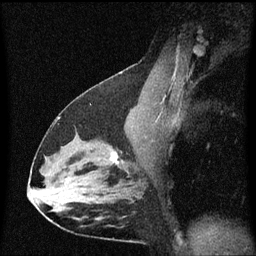
Breast MRI (dynamic contrast-enhanced), one sagittal slice; position 35 of 60 along the scan axis; dynamic contrast-enhanced series, image 2 of 3 at this slice position (ordered by acquisition); 1.5 T; TE 4.2 ms, TR 8.4 ms; 2 mm slice thickness; 256 × 256 image matrix, field of view 200 × 200 mm. Female patient, age 38 years. From the clinical record (not read from this slice): setting: breast cancer imaged before/during neoadjuvant chemotherapy; receptor status: HR-positive, HER2-negative.
Annotated regions visible in this slice (semi-automatic segmentation, software-assisted and operator-edited):
- analysis volume of interest (the breast-tissue region the enhancement analysis was run in; not a lesion): bounding box [x1, y1, x2, y2] px = [94, 138, 141, 185]
- tumour enhancement mask (voxels above the 70 % enhancement threshold inside the analysis volume of interest): [112, 154, 119, 163]